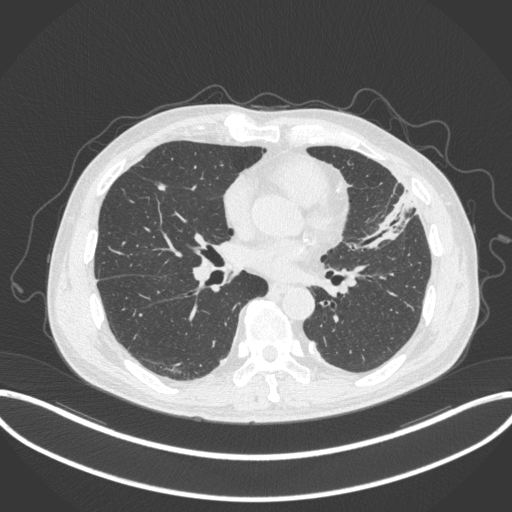
Chest CT, one axial slice; slice 154 of 382 in the series (ordered by position); reconstruction kernel B31f; lung window (W 1500 / L -600 HU); 1 mm slice thickness; 512 × 512 image matrix, field of view 415 × 415 mm. Patient: male, 64 years. From the clinical record (not read from this slice): clinical TNM (as recorded): T4 N1 M0.
Annotated regions visible in this slice (rectangle marked by the reading radiologist):
- lung tumour (recorded histology: adenocarcinoma): bounding box (x1, y1, x2, y2) in pixels: (364, 189, 416, 251)